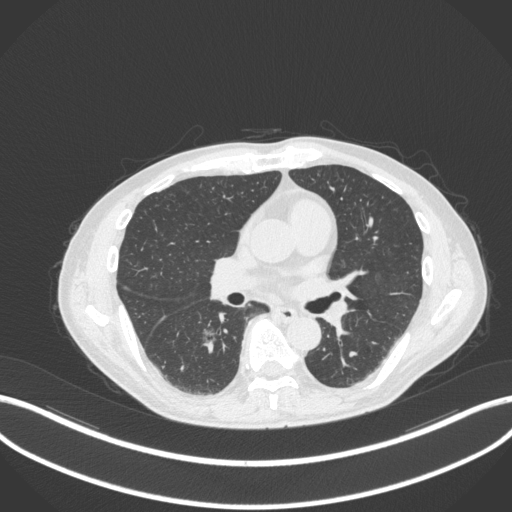
Chest CT, one axial slice; 120 kVp; lung window (W 1500 / L -600 HU); 512 × 512 image matrix. Male patient, age 61 years. From the clinical record (not read from this slice): clinical TNM (as recorded): T1c N0 M0.
Structures marked on this image (rectangle marked by the reading radiologist):
- lung tumour (recorded histology: adenocarcinoma): bounding box (x1, y1, x2, y2) in pixels: (198, 321, 219, 357)